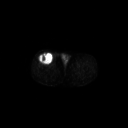
FDG PET of an extremity soft-tissue mass (from a PET/CT study), one axial slice. 128 × 128 image matrix, field of view 700 × 700 mm. Patient: male, 56 years. Case-level facts recorded for this patient, not image findings: histological type: pleiomorphic leiomyosarcoma; grade: intermediate; site of the primary tumour: right thigh.
Outlined on this slice (expert contour drawn on MRI and transferred to this co-registered scan by the dataset authors):
- gross tumour volume including surrounding oedema: bounding box [x1, y1, x2, y2] px = [38, 53, 54, 64]
- gross tumour volume (mass): [38, 53, 54, 64]